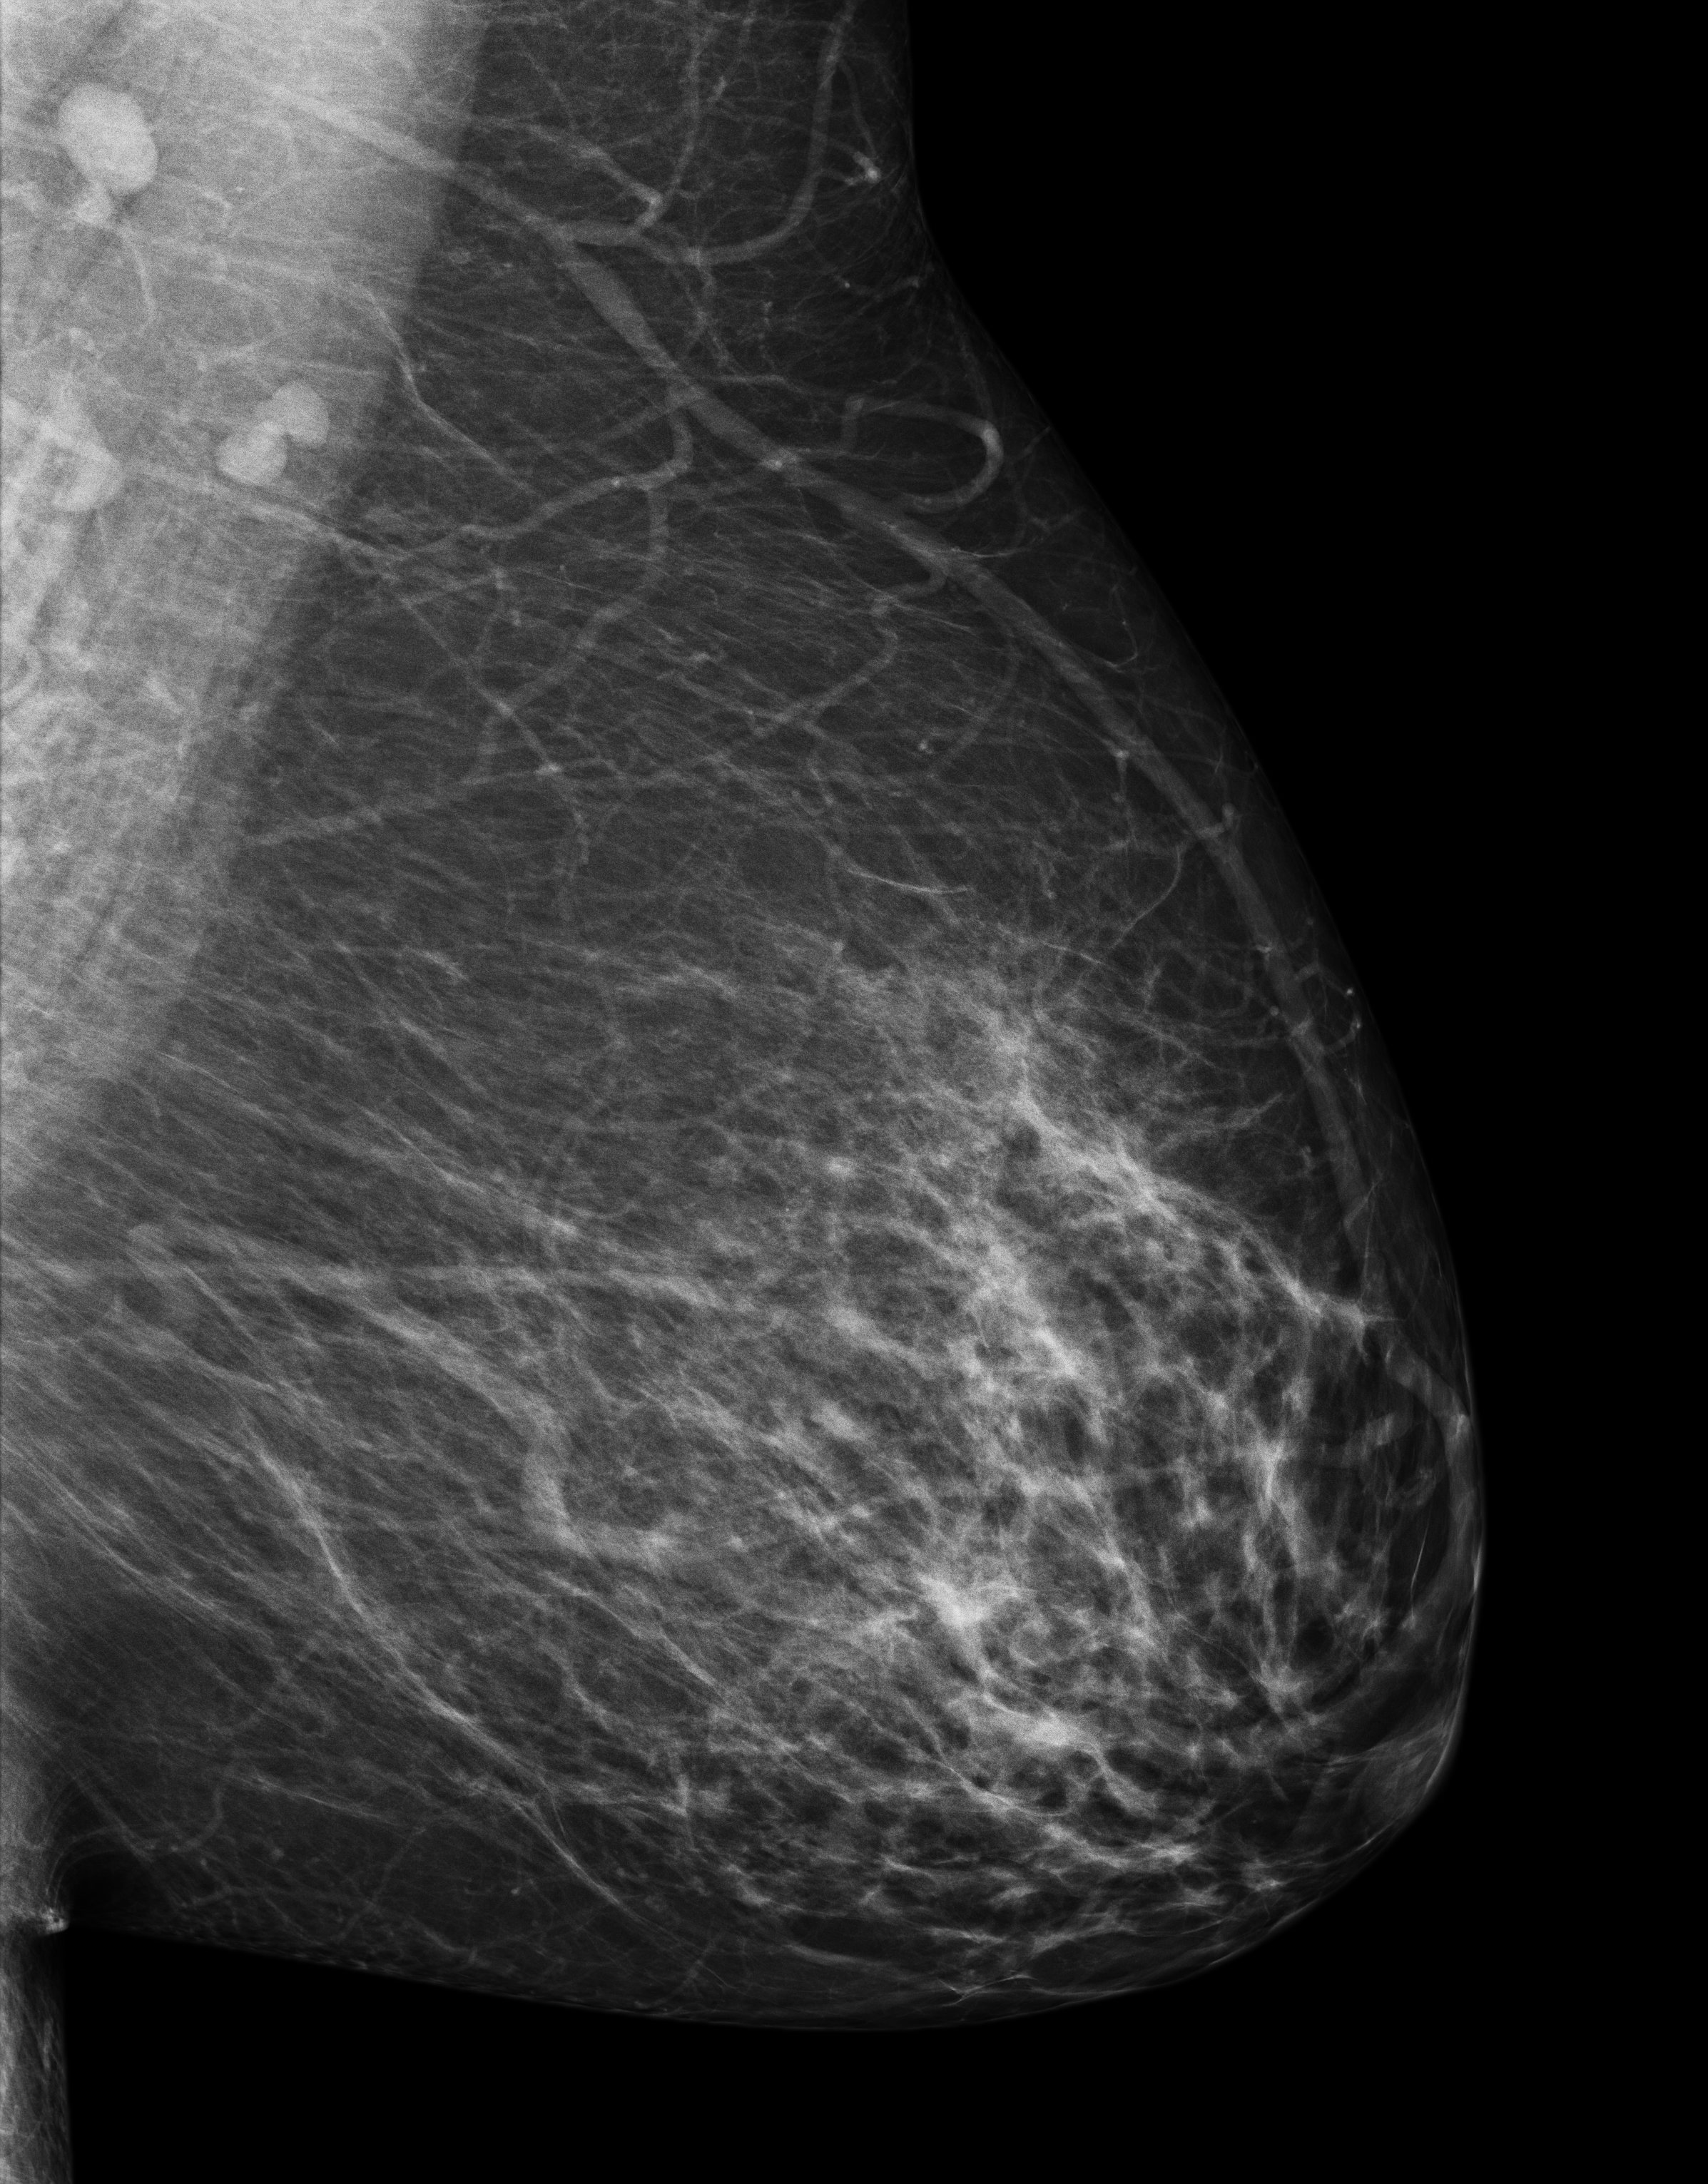
Screening examination, compressed breast thickness 92 mm, system: Senographe Essential ADS_56.21.3. Female patient, age 59 years.
Image type: full-field digital mammogram. Breast: left. Projection: mediolateral oblique (MLO) view.